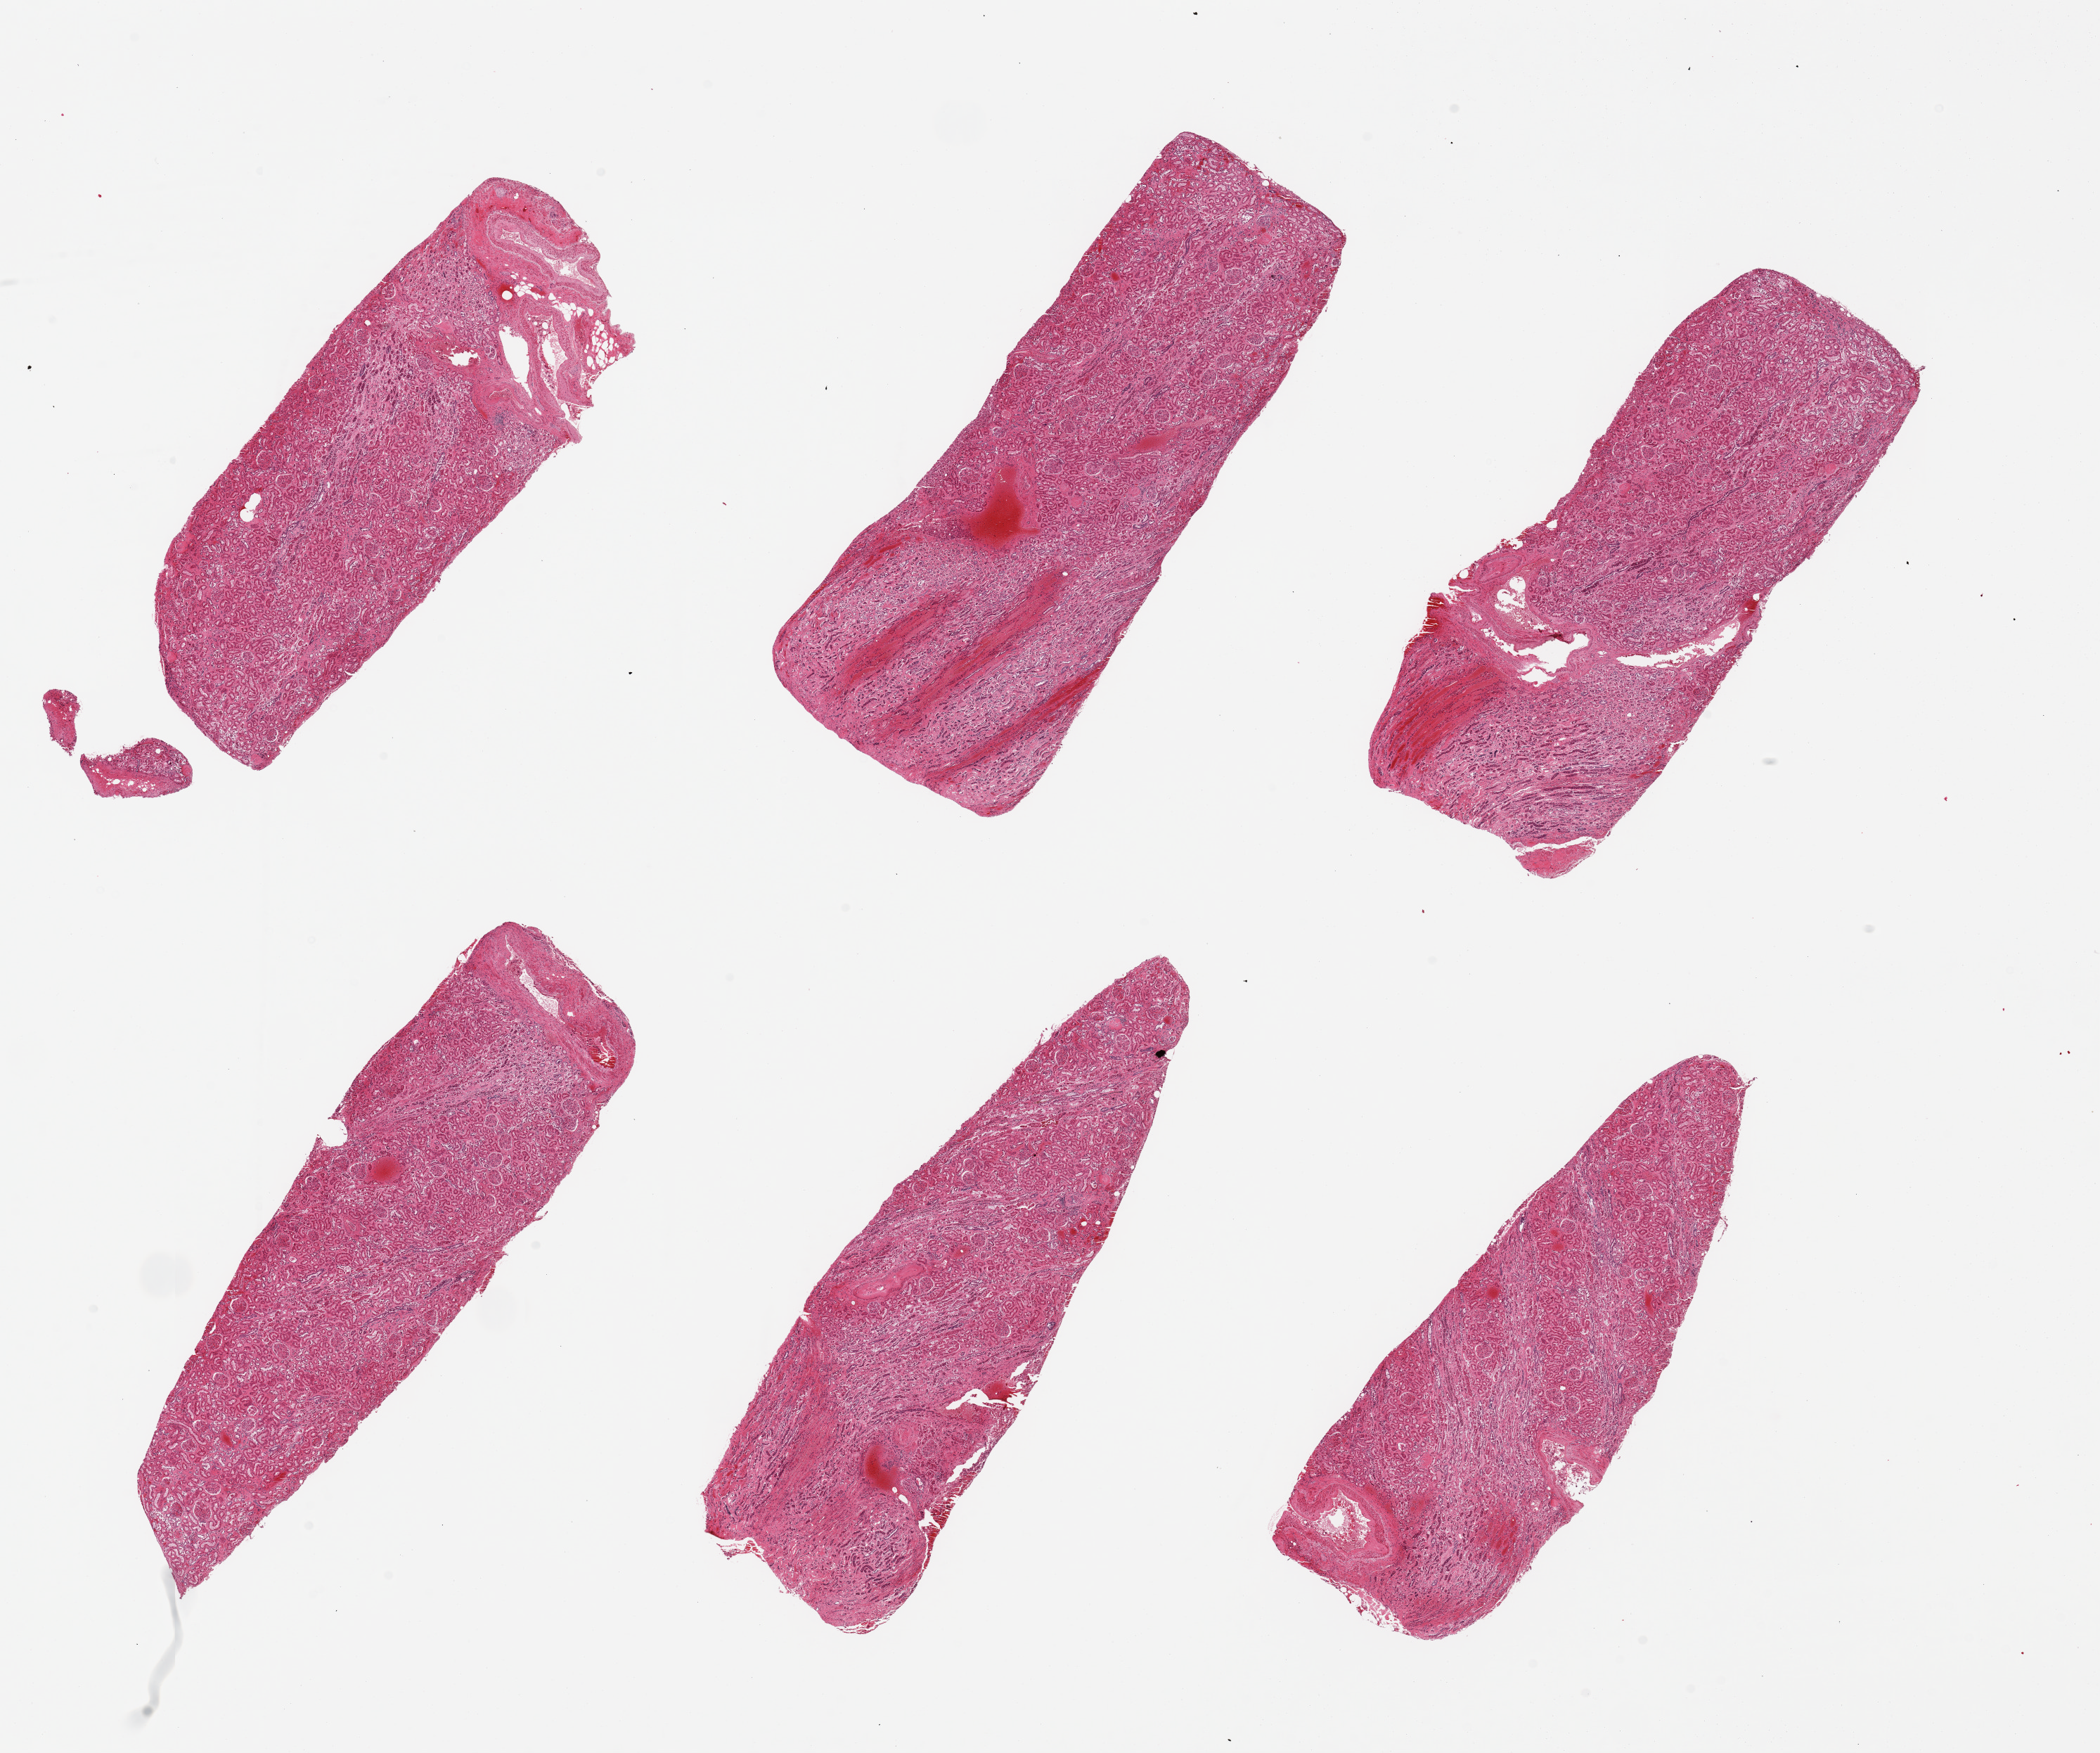
Whole-slide image, hematoxylin and eosin (H&E) stain, a low-resolution overview of the entire scanned area, about 23.6 x 19.7 mm; PAXgene-fixed, paraffin-embedded tissue; sampled site (target tissue): renal cortex; tissue donor sample. Donor sex: male.
Pathologist's review note for this sample: 6 pieces, up to 8x3mm, glomeruli present in all sections.